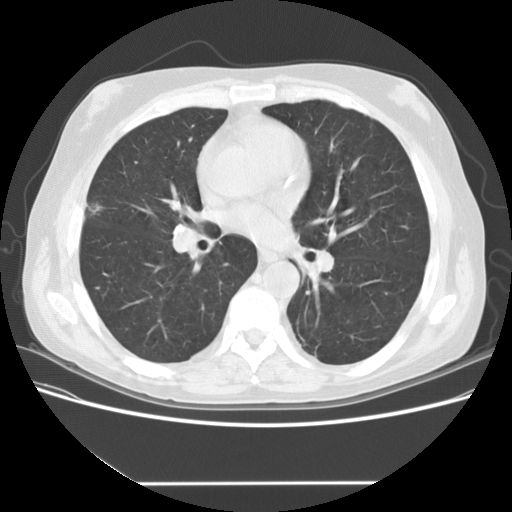
Low-dose screening chest CT, one axial slice; position 84 of 153 along the scan axis; reconstruction kernel STANDARD; lung window (W 1500 / L -600 HU); 2.5 mm slice thickness; 512 × 512 image matrix, field of view 360 × 360 mm.
Outlined on this slice (expert manual segmentation):
- lesion 2 (tumor, upper lobe of right lung): bounding box (x1, y1, x2, y2) in pixels: (88, 204, 103, 214)